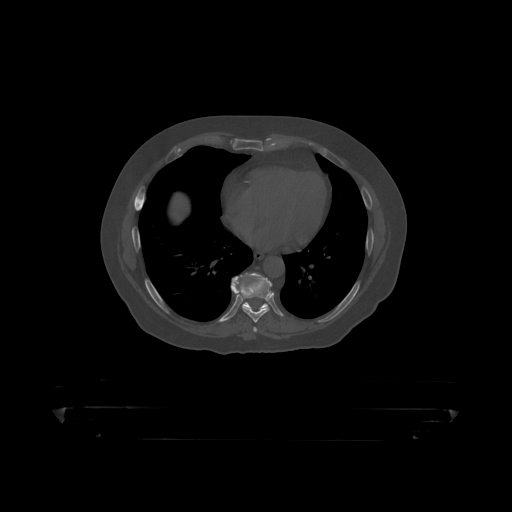
CT including the spine, one axial slice; position 252 of 390 along the scan axis; reconstruction kernel STANDARD; bone window (W 1800 / L 400 HU); 1.25 mm slice thickness; 512 × 512 image matrix, field of view 650 × 650 mm. Patient: male, 60 years. From the clinical record (not read from this slice): primary cancer: prostate.
Annotated regions visible in this slice (semi-automatic segmentation, software-assisted and operator-edited):
- T8 vertebra: bounding box [x1, y1, x2, y2] px = [232, 274, 273, 319]
- T9 vertebra: [231, 274, 268, 309]